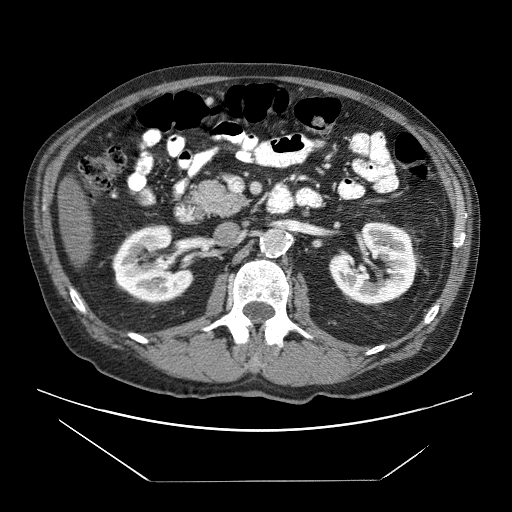
Contrast-enhanced abdominal CT (liver protocol), one axial slice. Position 12 of 83 along the scan axis. Reconstruction kernel STANDARD. 120 kVp. Soft-tissue window (W 400 / L 40 HU). 2.5 mm slice thickness. 512 × 512 image matrix. From the clinical record (not read from this slice): diagnosis: hepatocellular carcinoma (patient treated with transarterial chemoembolisation; whether this scan precedes or follows treatment is not stated here); TNM stage (as recorded): Stage-IVB; Child-Pugh class: B; tumour differentiation: poorly differentiated; tumour nodularity: uninodular.
Outlined on this slice (semi-automatically segmented with operator editing):
- liver parenchyma outside the tumour (the mass and vessels are separate outlines, so this box may not span the whole liver): bounding box <58,178,94,266> (left, top, right, bottom; pixels)